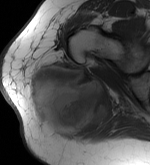
MRI of an extremity soft-tissue mass, one axial slice; MR volume resampled by the dataset authors to the PET/CT grid (not the native acquisition matrix); 150 × 165 image matrix, field of view 146 × 161 mm. Female patient. Case-level facts recorded for this patient, not image findings: histological type: epithelioid sarcoma with vascular differentiation; site of the primary tumour: right buttock.
Outlined on this slice (expert contour drawn on MRI and transferred to this co-registered scan by the dataset authors):
- gross tumour volume (mass): bounding box (x1, y1, x2, y2) in pixels: (28, 61, 111, 139)